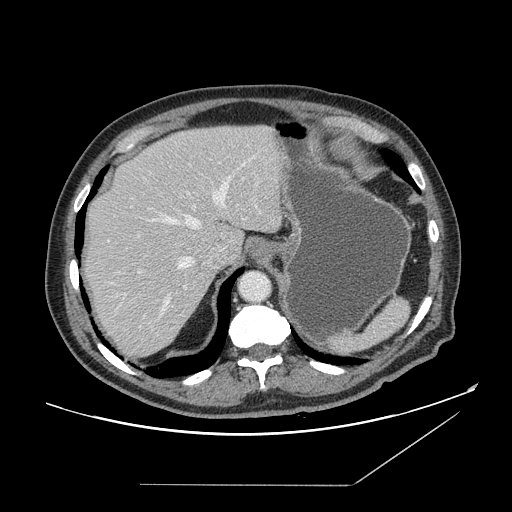
Contrast-enhanced abdominal CT, one axial slice. Position 121 of 166 along the scan axis. 120 kVp. Intravenous contrast given. Soft-tissue window (W 400 / L 40 HU). 2.5 mm slice thickness. 512 × 512 image matrix, field of view 416 × 416 mm. Male patient, age 80 years. From the clinical record (not read from this slice): diagnosis: colorectal cancer liver metastases, imaged before liver resection; multiple liver metastases: no; largest metastasis: 2.2 cm; disease in both lobes: no.
Annotated regions visible in this slice (manually delineated by an expert):
- hepatic veins: box from (x=160, y=178) to (x=231, y=316) px
- liver: (x=82, y=125)–(x=282, y=357)
- planned liver remnant (the part of the liver to remain after resection): (x=85, y=125)–(x=283, y=255)
- portal vein (with intrahepatic branches): (x=139, y=206)–(x=195, y=273)